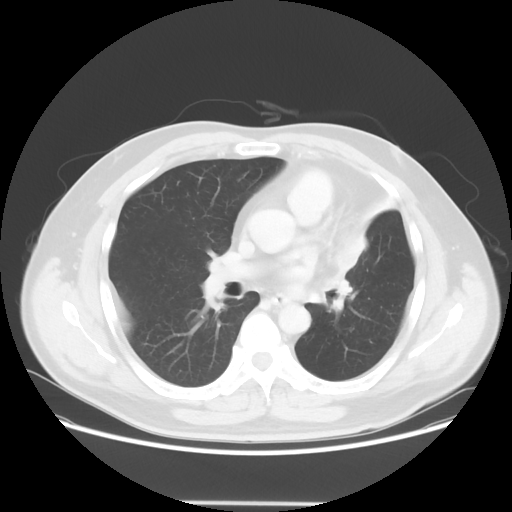
Chest CT, one axial slice; slice 34 of 62 in the series (ordered by position); reconstruction kernel STANDARD; 120 kVp; lung window (W 1500 / L -600 HU); 5 mm slice thickness; 512 × 512 image matrix, field of view 403 × 403 mm. Patient: male, 49 years. Case-level facts recorded for this patient, not image findings: clinical TNM (as recorded): T3 N3 M1c.
Outlined on this slice (rectangle marked by the reading radiologist):
- lung tumour (recorded histology: squamous cell carcinoma): box from (x=314, y=240) to (x=372, y=313) px